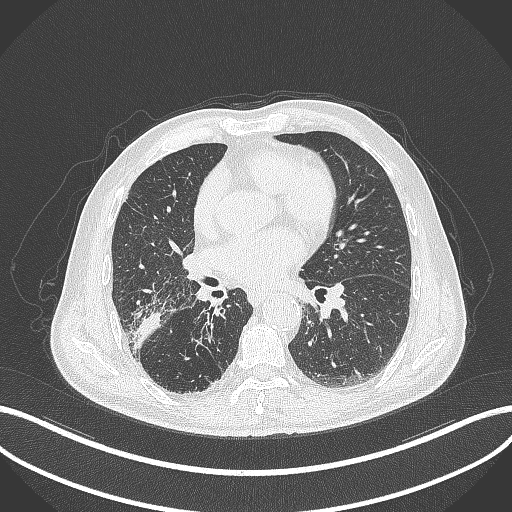
Chest CT, one axial slice. Slice 202 of 429 in the series (ordered by position). Reconstruction kernel B70f. Lung window (W 1500 / L -600 HU). 512 × 512 image matrix. Patient: male, 72 years. Case-level facts recorded for this patient, not image findings: clinical TNM (as recorded): T3 N2 M0.
Annotated regions visible in this slice (rectangle marked by the reading radiologist):
- lung tumour (recorded histology: adenocarcinoma): bounding box (x1, y1, x2, y2) in pixels: (129, 314, 162, 349)